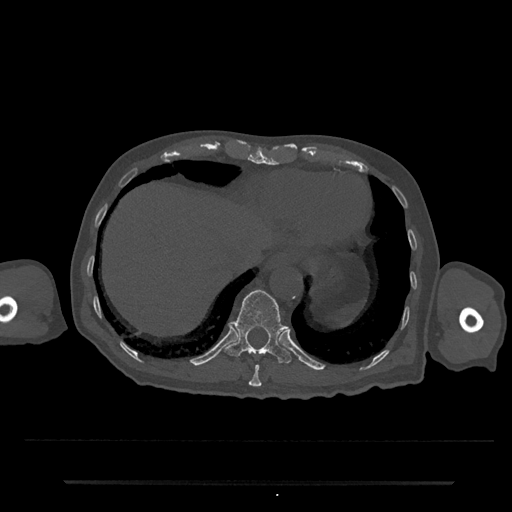
CT including the spine, one axial slice. Position 267 of 797 along the scan axis. Reconstruction kernel Br40s/3. Bone window (W 1800 / L 400 HU). 512 × 512 image matrix. Male patient, age 74 years. From the clinical record (not read from this slice): primary cancer: prostate.
Annotated regions visible in this slice (semi-automatically segmented with operator editing):
- T10 vertebra: box from (x=249, y=364) to (x=262, y=387) px
- T11 vertebra: (x=224, y=290)–(x=292, y=364)